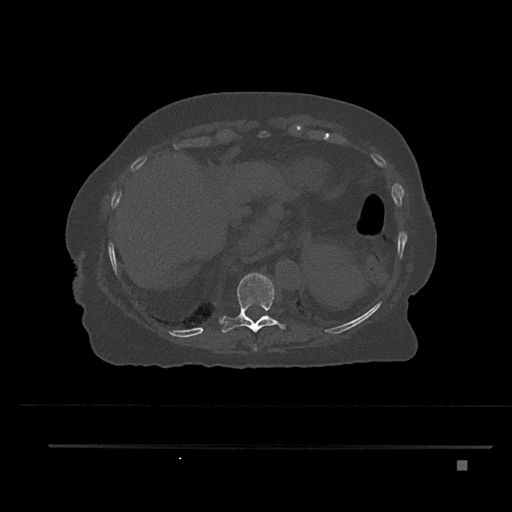
CT including the spine, one axial slice; slice 355 of 797 in the series (ordered by position); bone window (W 1800 / L 400 HU); 0.5 mm slice thickness; 512 × 512 image matrix, field of view 437 × 437 mm. Female patient, age 76 years. Case-level facts recorded for this patient, not image findings: primary cancer: lung; vertebrae with lytic lesions (as recorded): T11, L3.
Outlined on this slice (semi-automatic segmentation, software-assisted and operator-edited):
- T10 vertebra: box from (x=220, y=273) to (x=286, y=333) px
- T9 vertebra: (x=253, y=343)–(x=258, y=352)